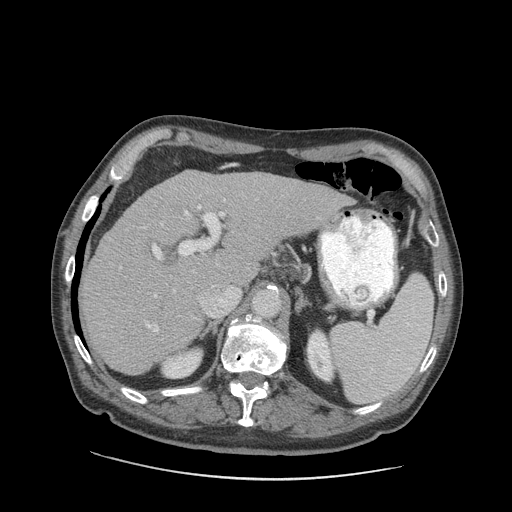
Contrast-enhanced abdominal CT (liver protocol), one axial slice; position 58 of 89 along the scan axis; reconstruction kernel STANDARD; soft-tissue window (W 400 / L 40 HU); 2.5 mm slice thickness; 512 × 512 image matrix, field of view 420 × 420 mm. Case-level facts recorded for this patient, not image findings: diagnosis: hepatocellular carcinoma (patient treated with transarterial chemoembolisation; whether this scan precedes or follows treatment is not stated here); TNM stage (as recorded): Stage-I; Child-Pugh class: A; tumour size: 4.6 cm.
Structures marked on this image (semi-automatic segmentation, software-assisted and operator-edited):
- liver parenchyma outside the tumour (the mass and vessels are separate outlines, so this box may not span the whole liver): bounding box [x1, y1, x2, y2] px = [80, 170, 350, 374]
- liver vessels: [103, 187, 319, 337]